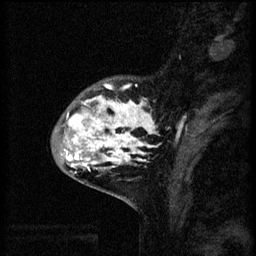
Breast MRI (dynamic contrast-enhanced), one sagittal slice. Slice 16 of 60 in the series (ordered by position). 3 images stored at this slice position (order not interpretable as contrast timing). 1.5 T. TE 4.2 ms, TR 8.2 ms. 2 mm slice thickness. 256 × 256 image matrix. Patient: female, 41 years.
Structures marked on this image (semi-automatic segmentation, software-assisted and operator-edited):
- analysis volume of interest (the breast-tissue region the enhancement analysis was run in; not a lesion): bounding box [x1, y1, x2, y2] px = [53, 78, 160, 175]
- tumour enhancement mask (voxels above the 70 % enhancement threshold inside the analysis volume of interest): [64, 84, 158, 171]